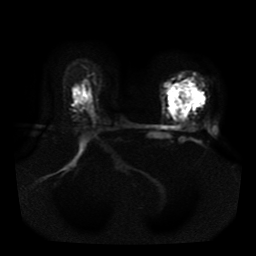
Breast MRI, one axial slice; diffusion-weighted series; image 2 of 4 stored at this slice position (different b-values; order by instance number); 1.5 T; 256 × 256 image matrix, field of view 330 × 330 mm. Female patient.
Annotated regions visible in this slice (expert manual segmentation):
- tumour on diffusion-weighted imaging: bounding box <169,84,203,120> (left, top, right, bottom; pixels)